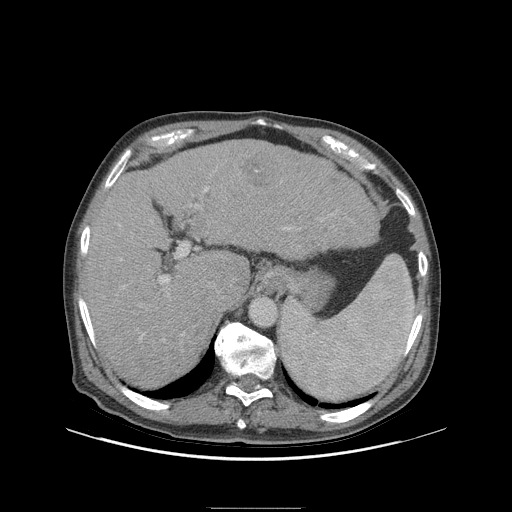
Contrast-enhanced abdominal CT (liver protocol), one axial slice; slice 69 of 105 in the series (ordered by position); soft-tissue window (W 400 / L 40 HU); 512 × 512 image matrix, field of view 440 × 440 mm. Case-level facts recorded for this patient, not image findings: diagnosis: hepatocellular carcinoma (patient treated with transarterial chemoembolisation; whether this scan precedes or follows treatment is not stated here); TNM stage (as recorded): Stage-I; Child-Pugh class: A; tumour size: 5.1 cm.
Structures marked on this image (semi-automatic segmentation, software-assisted and operator-edited):
- liver parenchyma outside the tumour (the mass and vessels are separate outlines, so this box may not span the whole liver): bounding box <82,140,378,388> (left, top, right, bottom; pixels)
- mass: <239,150,279,189>
- liver vessels: <90,187,290,345>